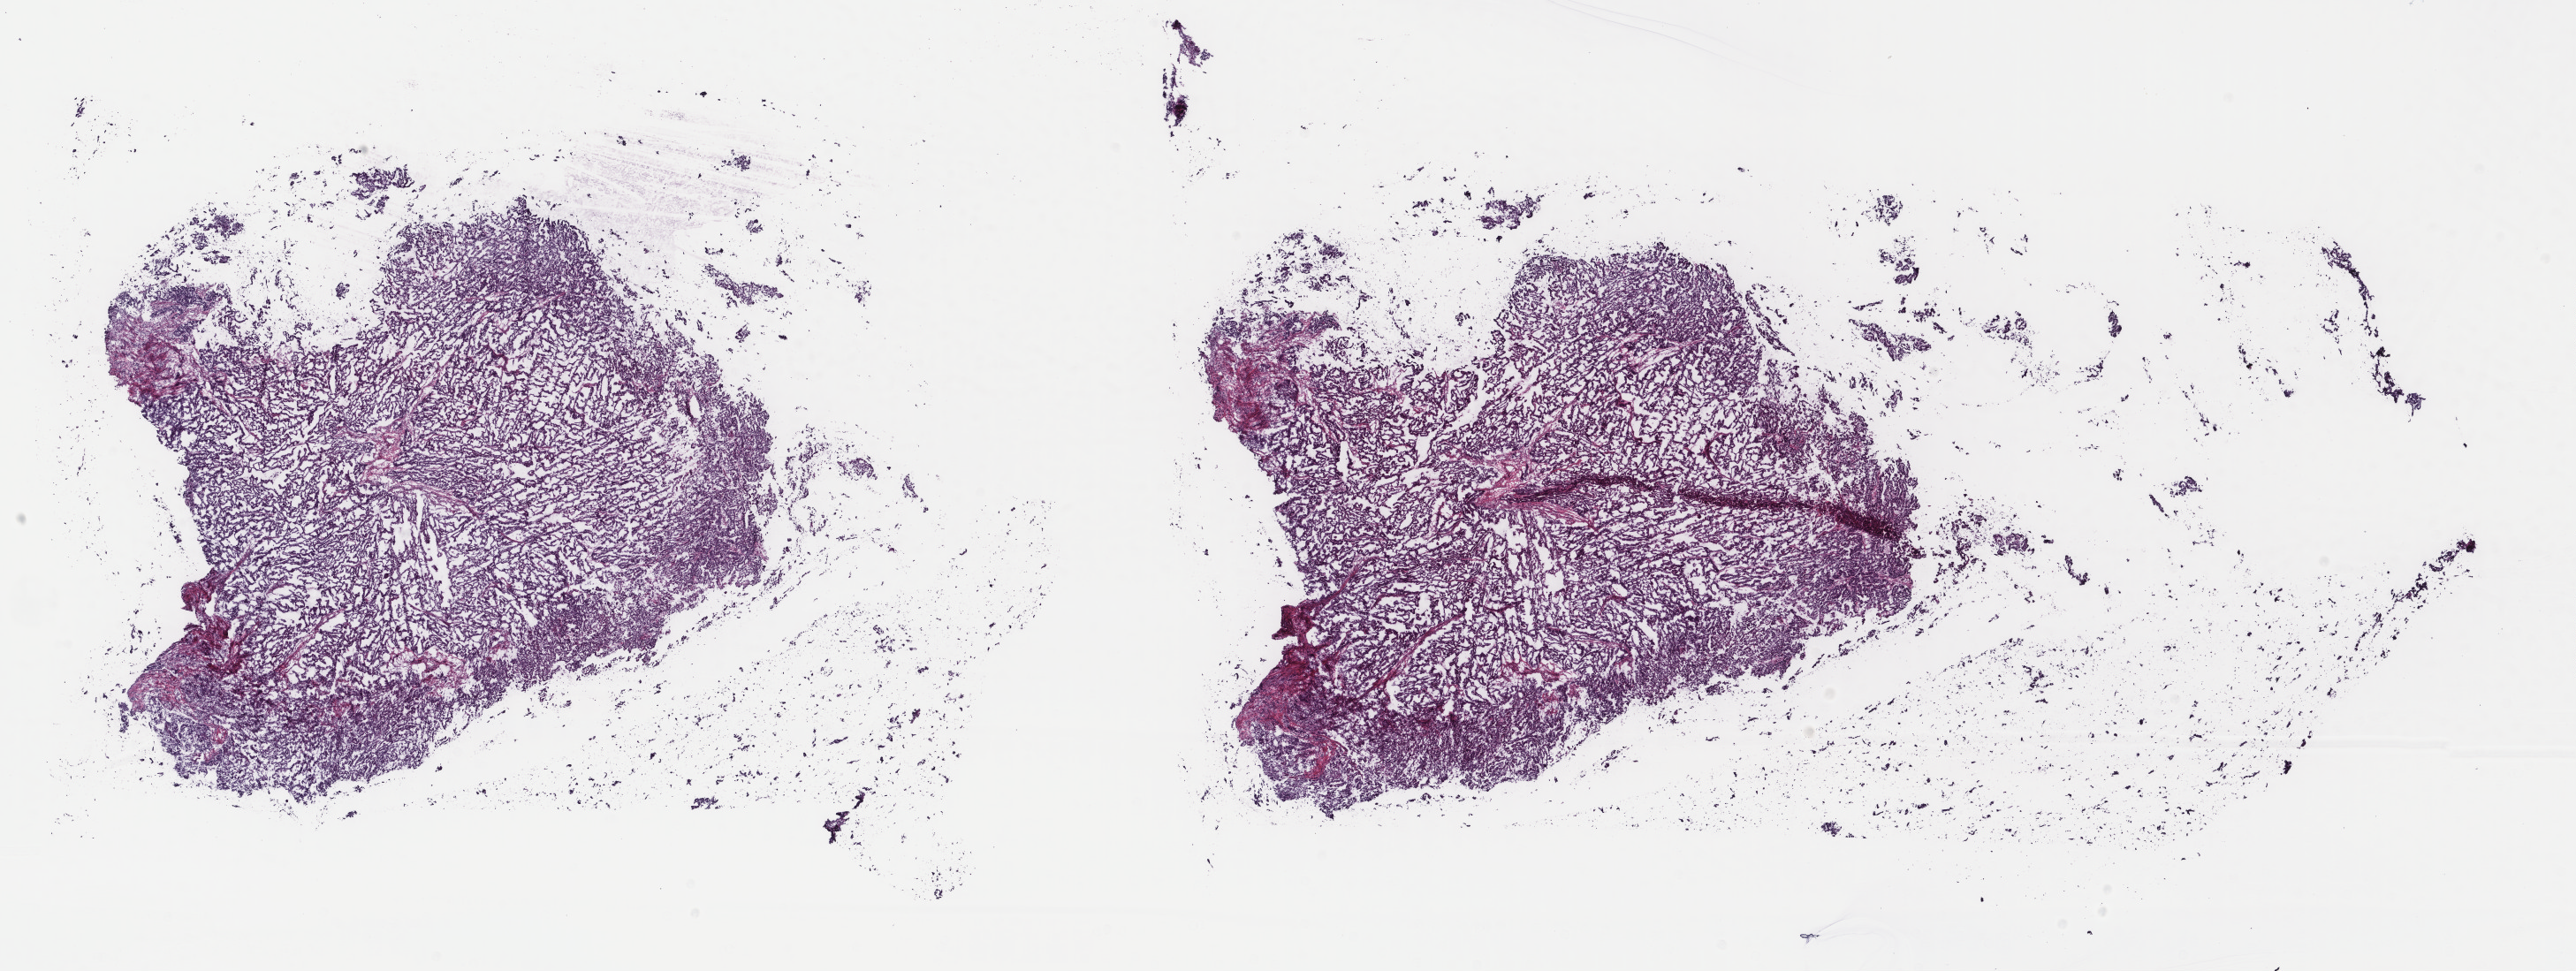
Hematoxylin and eosin (H&E) stained whole-slide image, a low-resolution overview of the entire scanned area, about 23.1 x 8.7 mm, frozen section, primary tumour sample from the uterus. Female, age 70 years at initial diagnosis.
Diagnosis: Serous cystadenocarcinoma, NOS (endometrium).